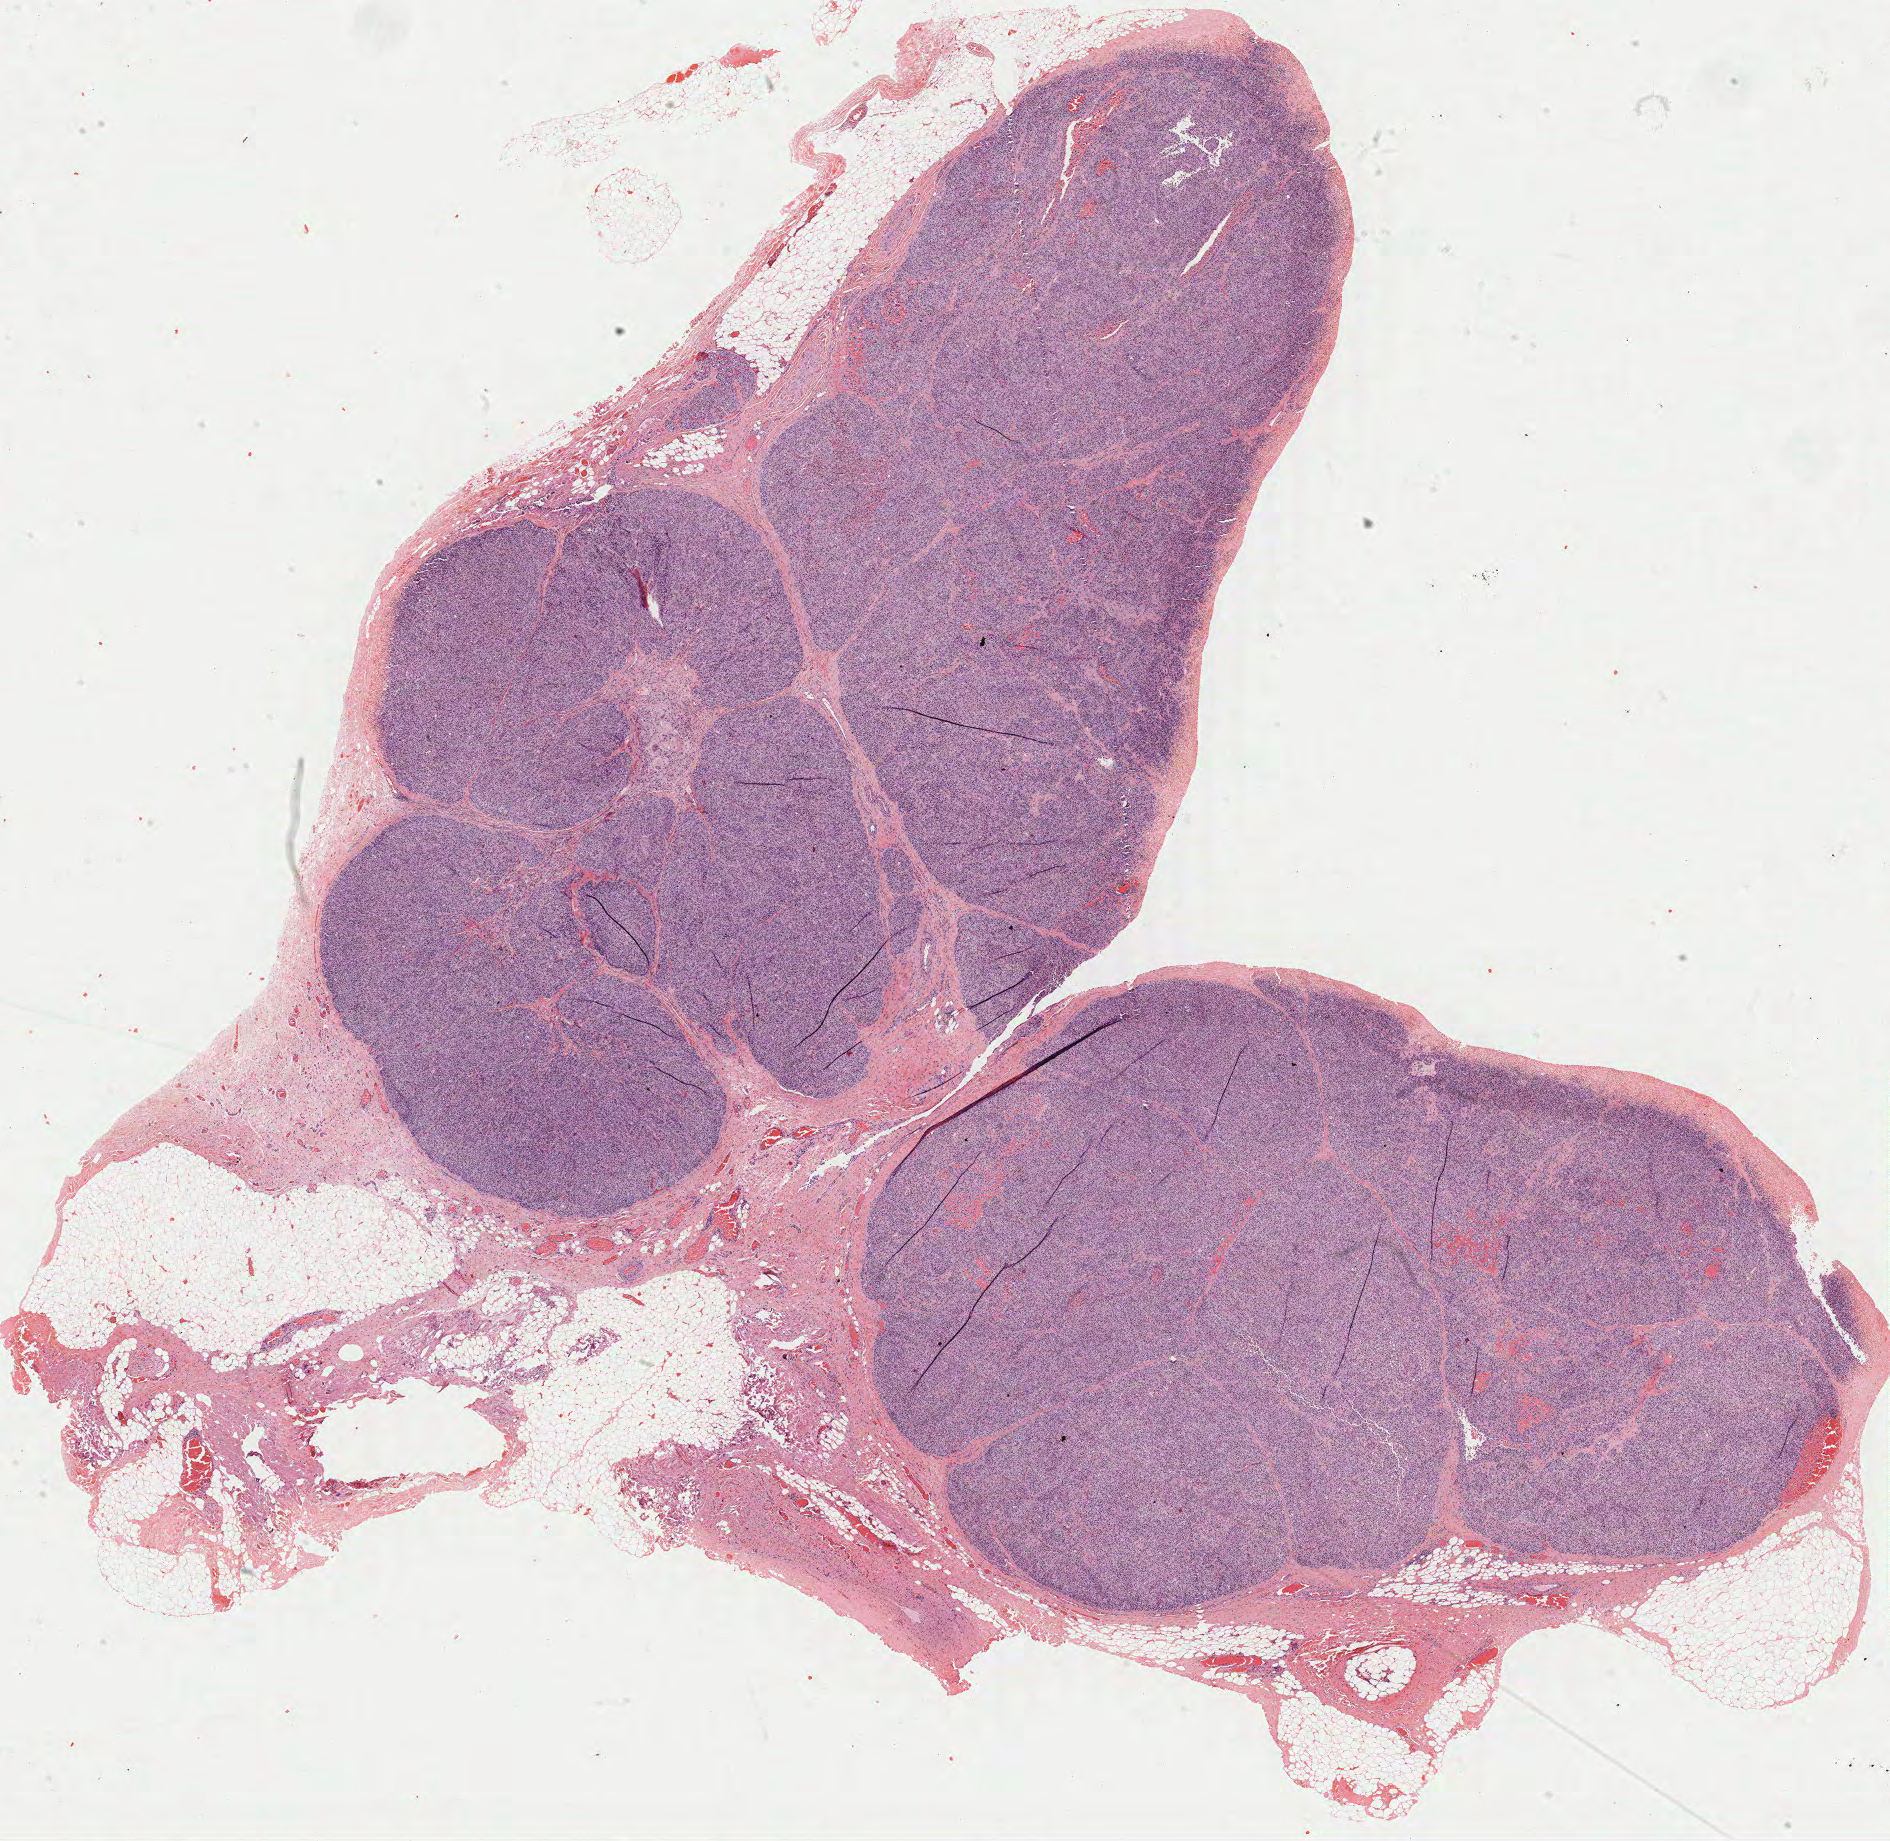
Whole-slide histology image, Hematoxylin and eosin (H&E) stained — whole scanned area (about 15.2 x 14.8 mm, from a 40x scan) shown as a low-resolution overview; FFPE section; metastatic tumour sample, sampled site not recorded. Male patient; age at initial diagnosis 43 years.
• this section: metastatic tumour tissue
• patient diagnosis: Malignant melanoma, NOS